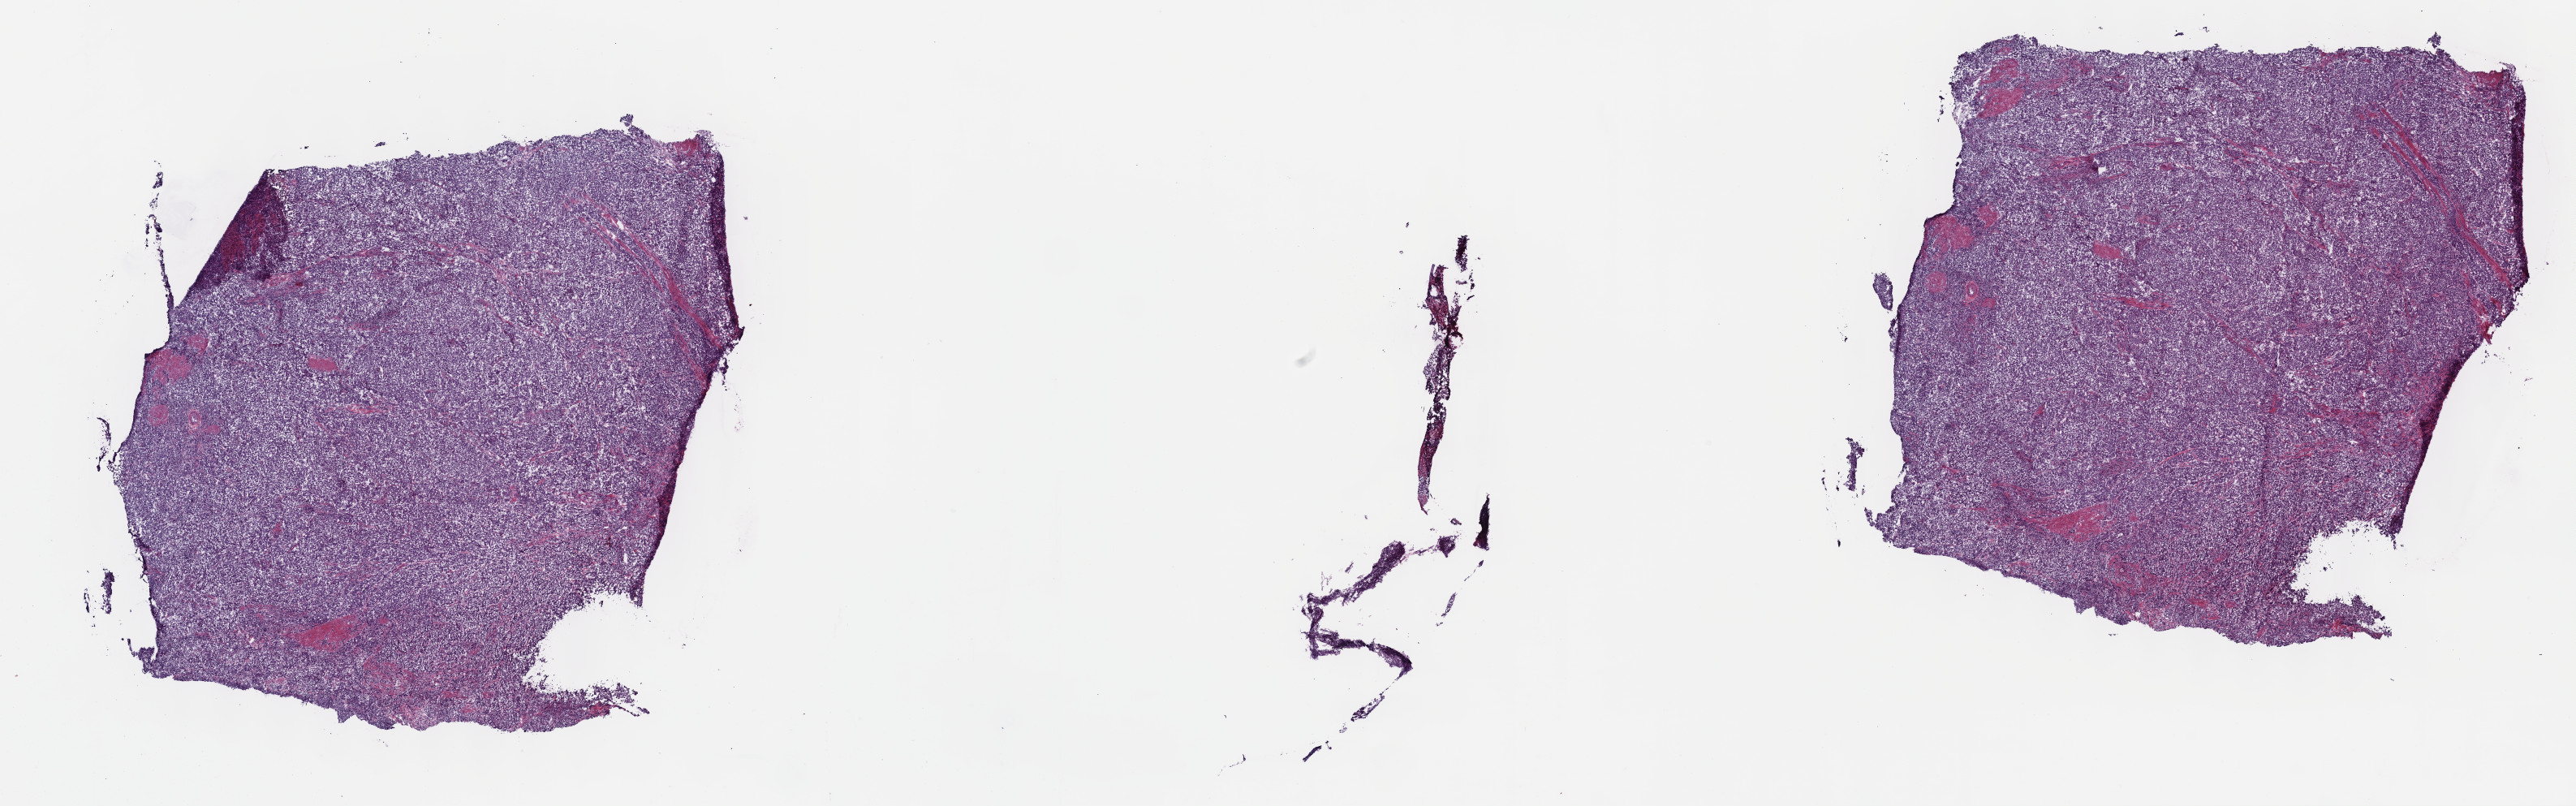
H&E-stained whole-slide image — whole scanned area (about 25.7 x 8.0 mm, slide scanned at 40x) shown as a low-resolution overview. Frozen section. Bladder, primary tumour sample. Patient: male, age at initial diagnosis 55 years. Histologic grade: high grade. Slide review estimates, as recorded: tumour cells 100%, tumour nuclei 80%, normal cells 0%, stromal cells 0%, necrosis 0%. Inflammatory infiltration, as recorded: lymphocyte infiltration 2%, monocyte infiltration 0%, neutrophil infiltration 0%.
AJCC pathologic stage: II (7th edition). Histologic diagnosis: Transitional cell carcinoma (lateral wall of bladder). Lymph nodes positive (case pathology): 0 of 16 examined.